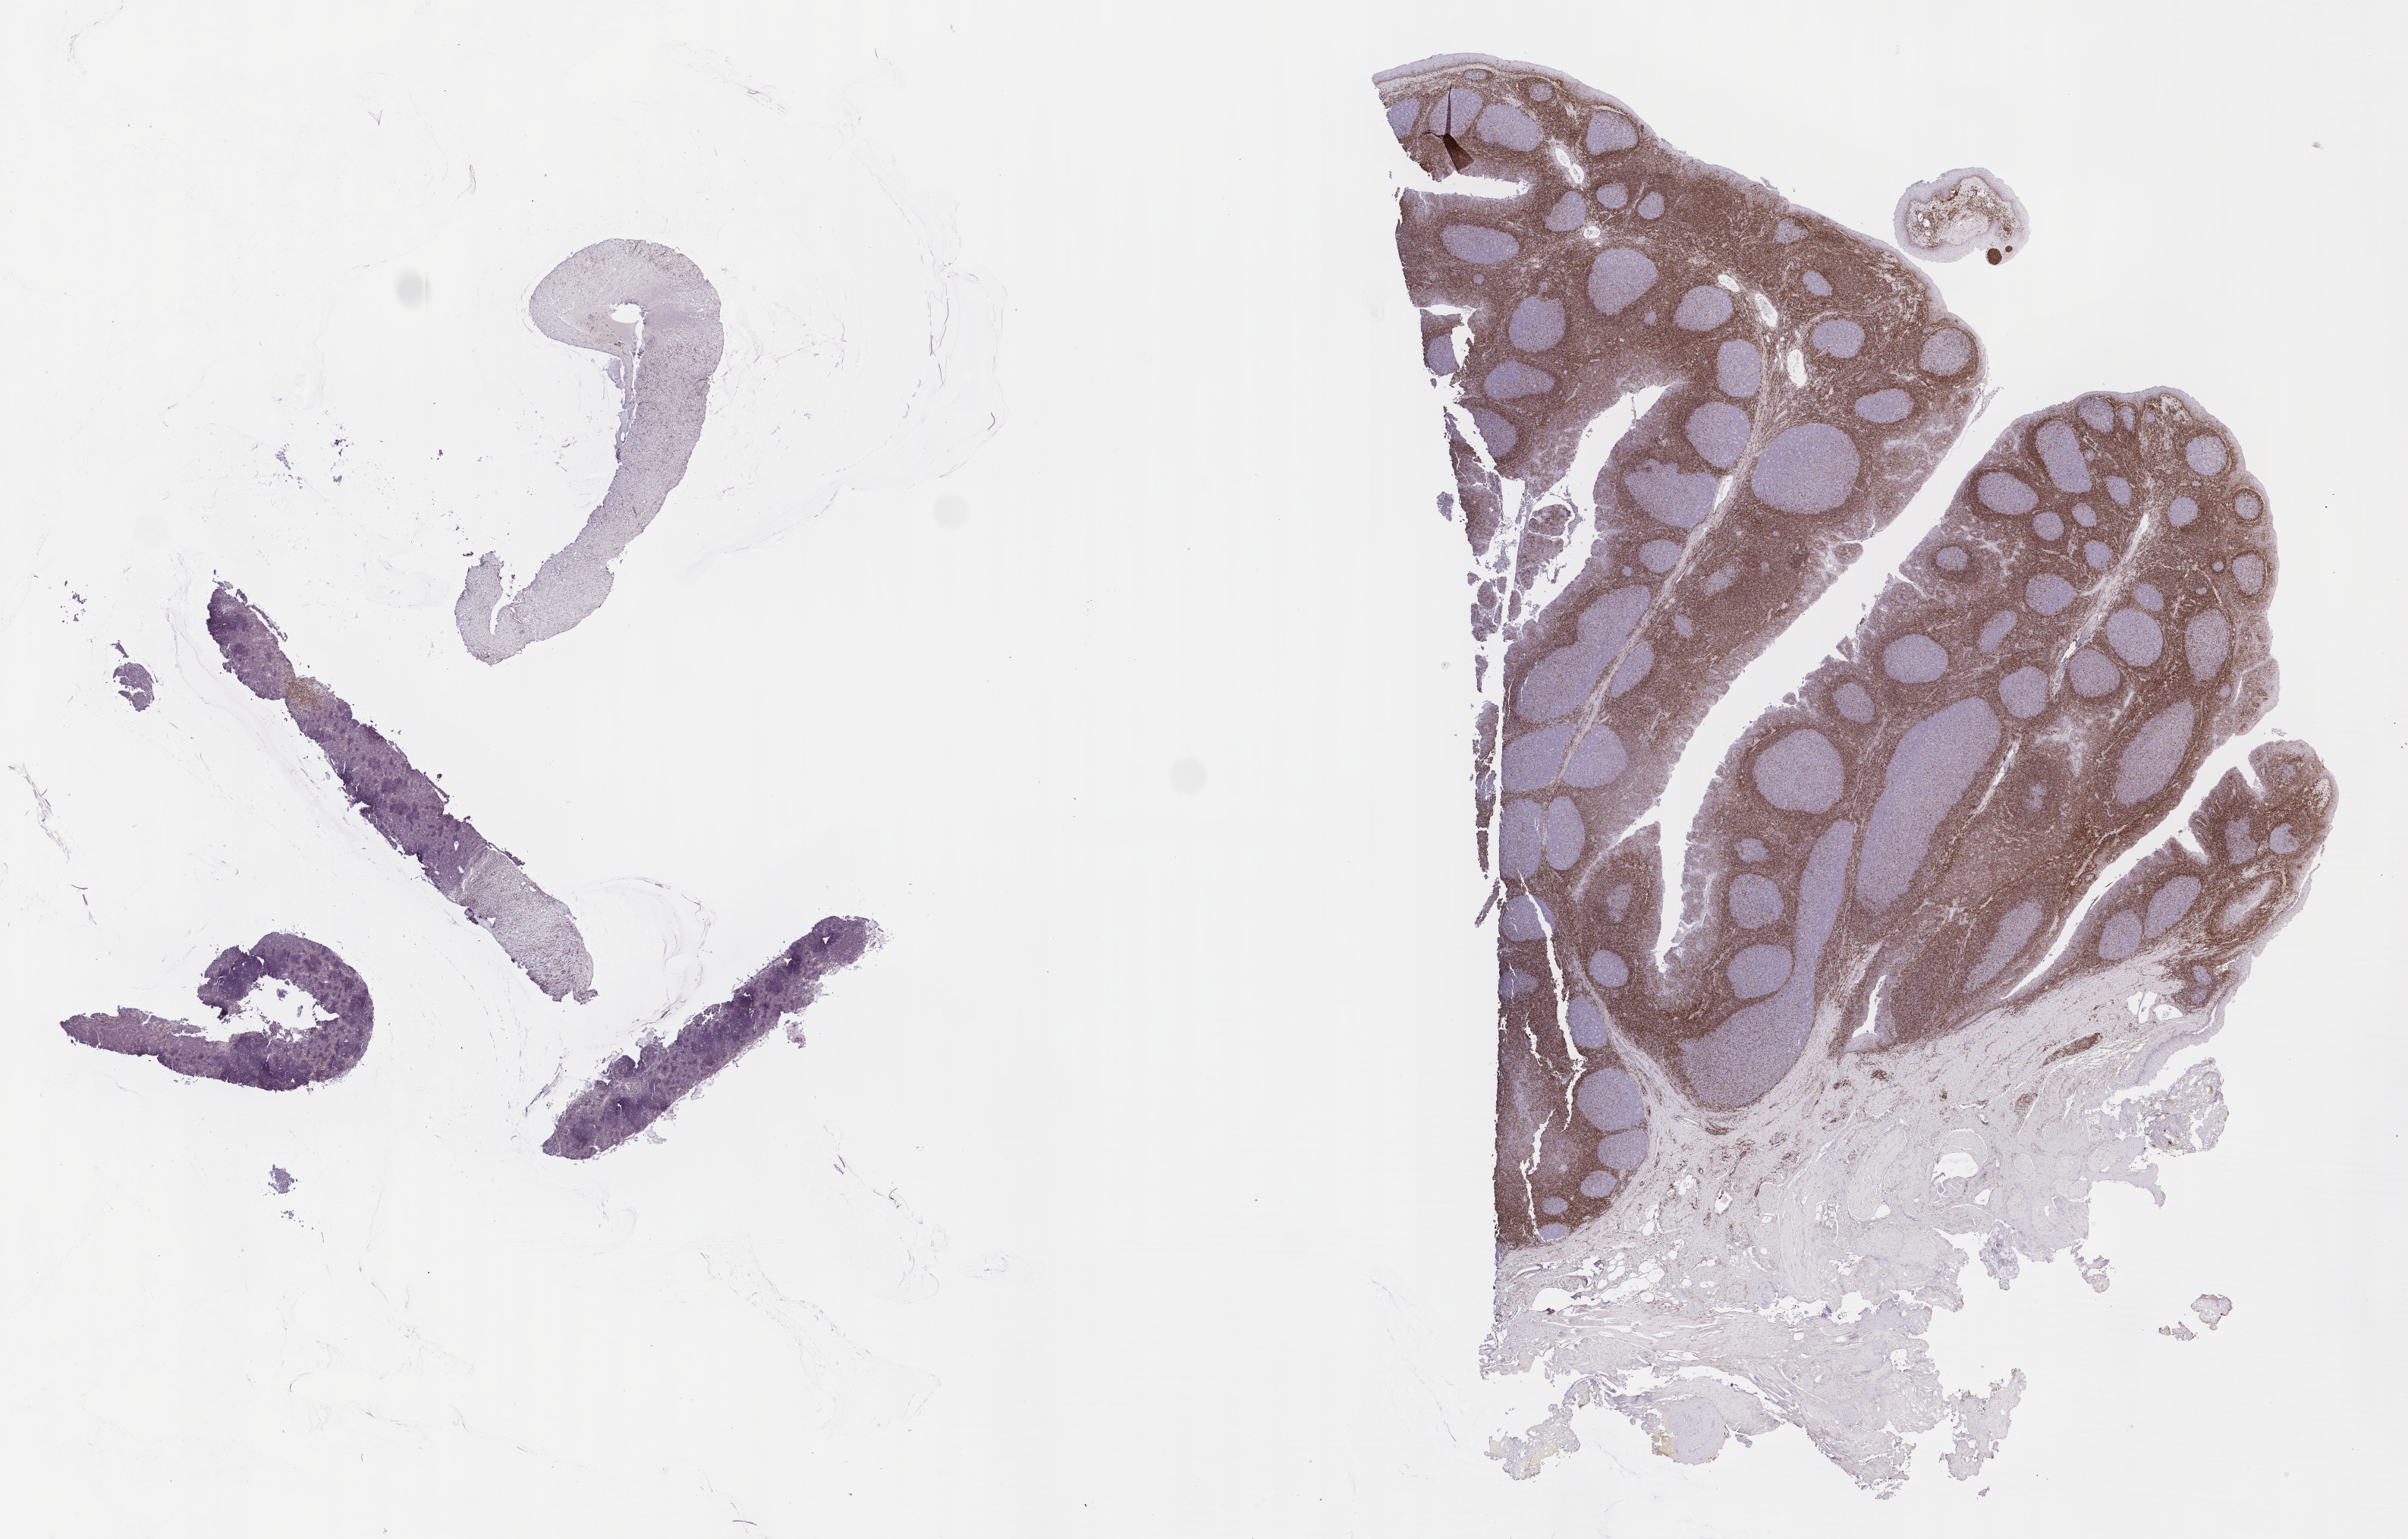
IHC for BCL2, whole-slide image — a low-resolution overview of the entire scanned area, about 25.7 x 16.4 mm. Patient sex: male.
• specimen: tumor tissue